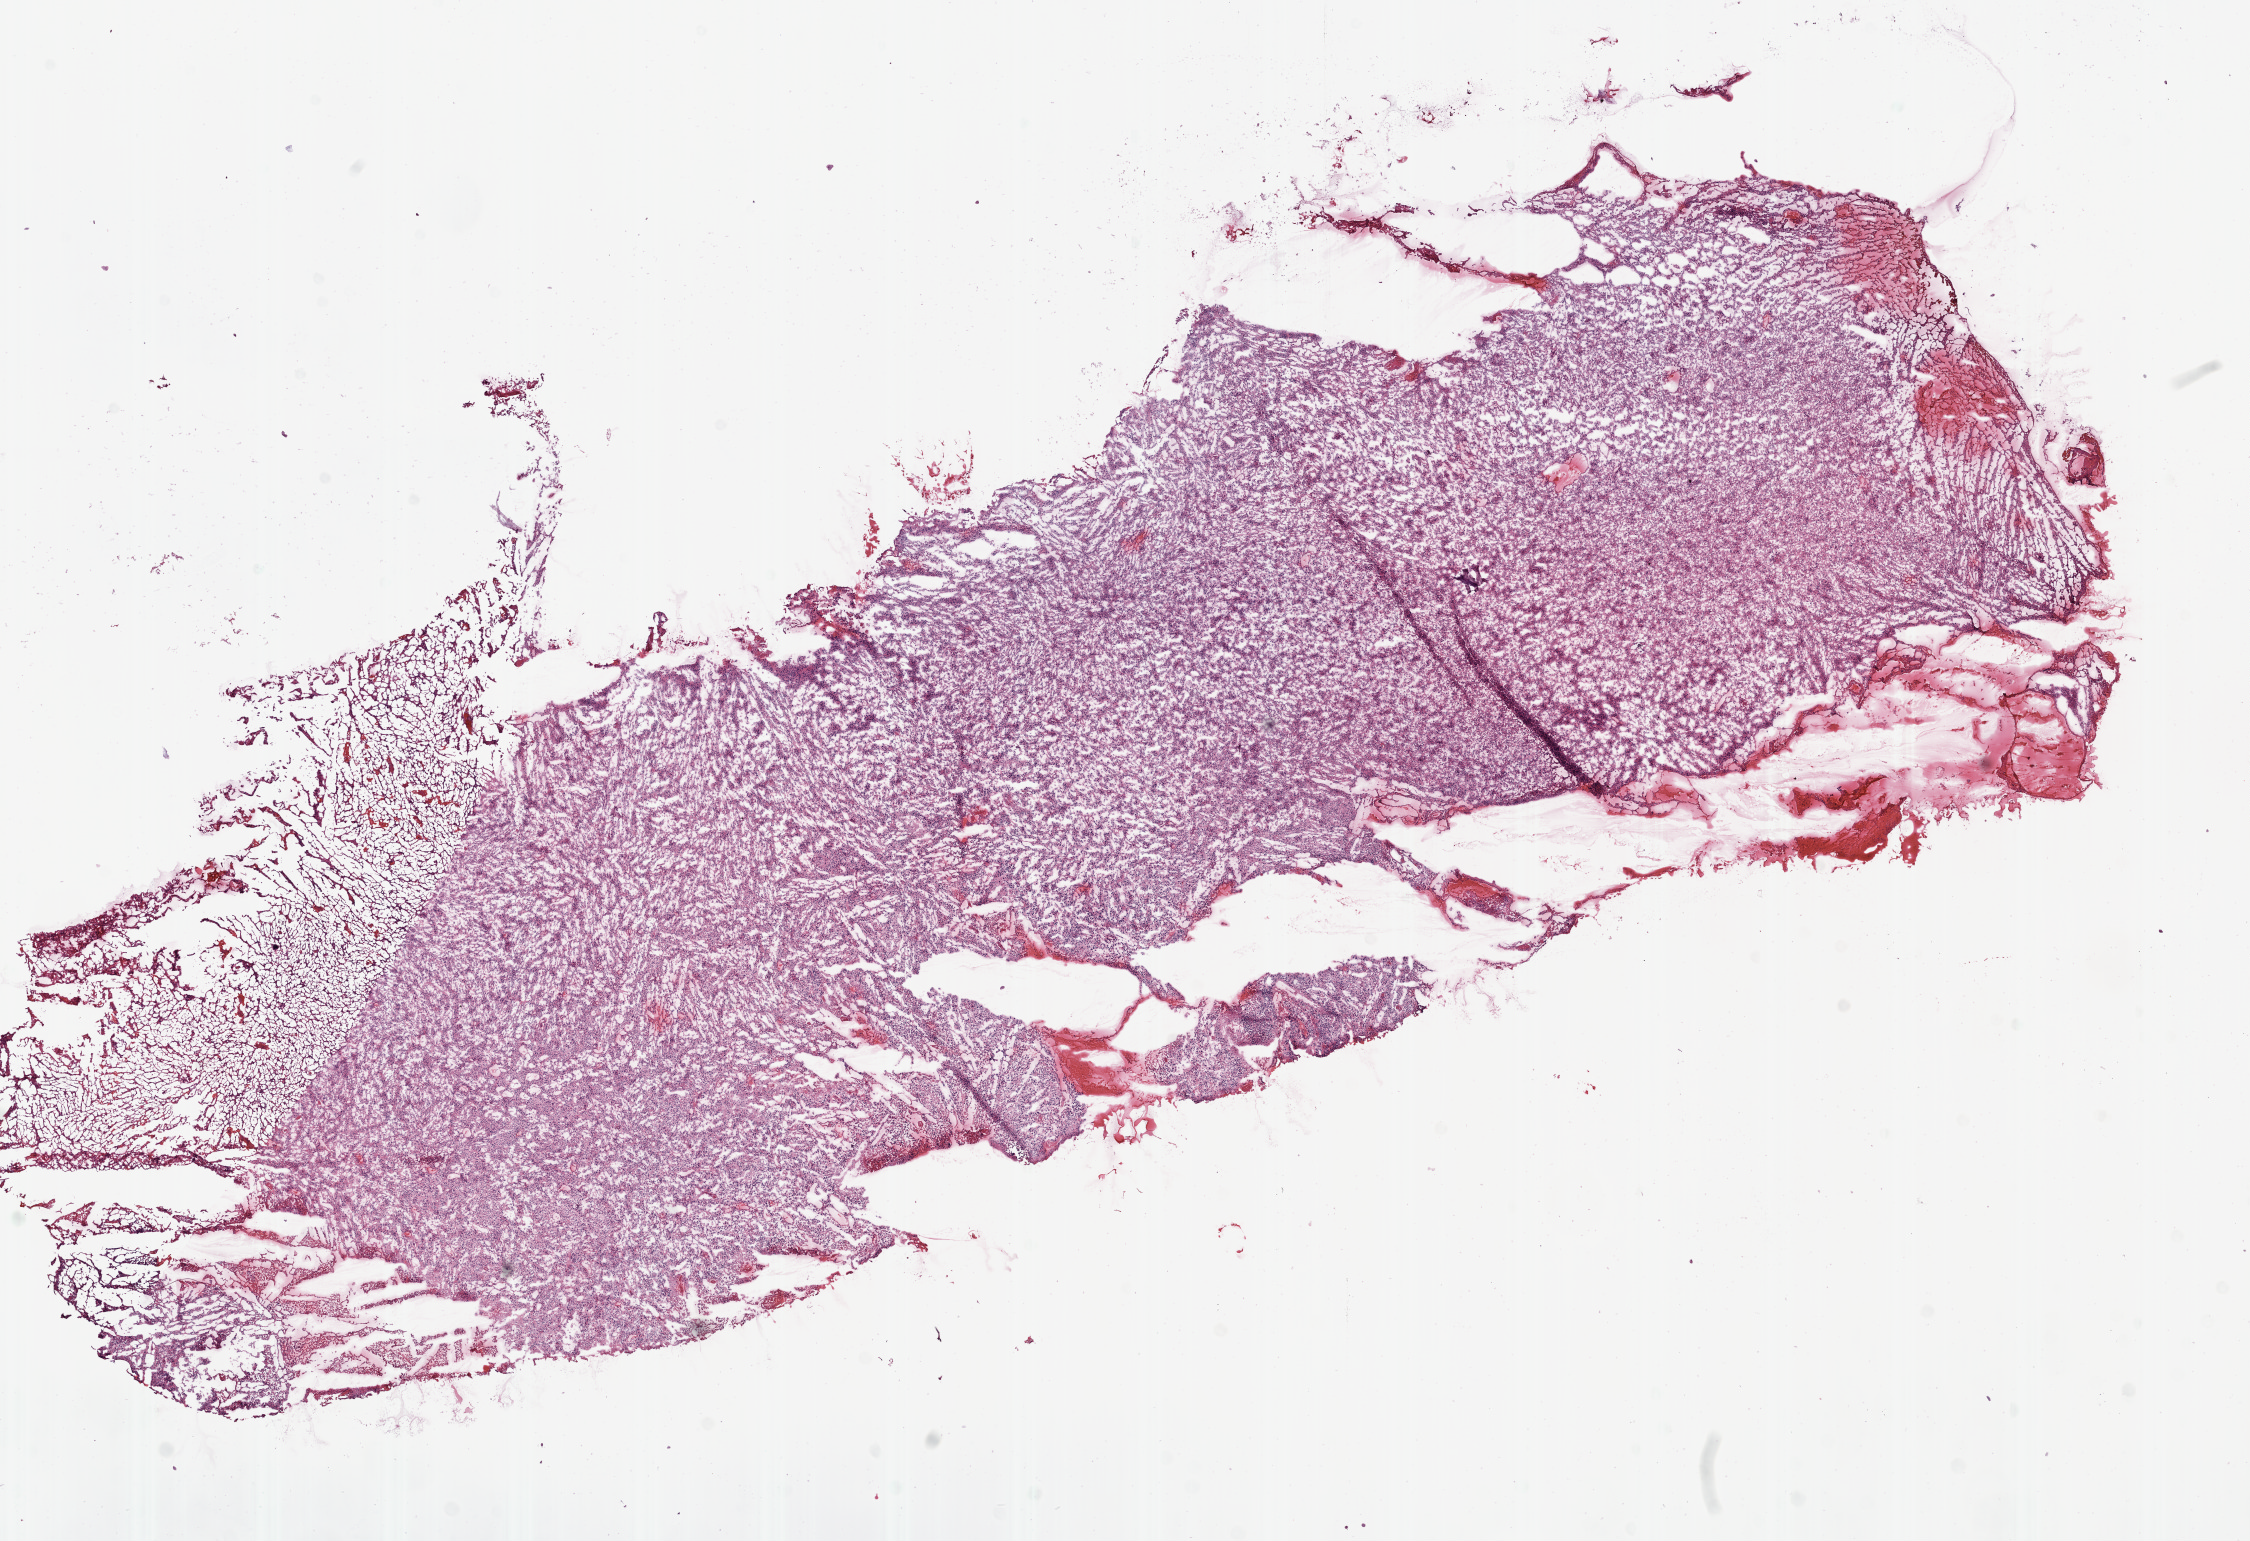
H&E-stained whole-slide image — shown as a low-resolution overview of the whole scanned area (about 18.1 x 12.4 mm, acquisition: 20x scan), frozen section, primary tumour sample from the brain. Female, age 50 years at initial diagnosis. Pathologist review of this section (percent, as recorded): tumour cells 100%, tumour nuclei 85%, normal cells 0%, stromal cells 0%, necrosis 0%.
• pathologic diagnosis: Glioblastoma